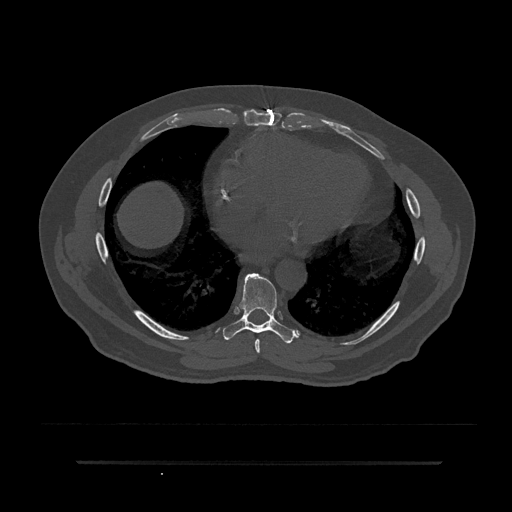
CT including the spine, one axial slice; slice 436 of 797 in the series (ordered by position); 120 kVp; bone window (W 1800 / L 400 HU); 0.5 mm slice thickness; 512 × 512 image matrix, field of view 464 × 464 mm. Patient: male, 59 years. Case-level facts recorded for this patient, not image findings: primary cancer: bile ducts.
Annotated regions visible in this slice (semi-automatic segmentation, software-assisted and operator-edited):
- T7 vertebra: bounding box (x1, y1, x2, y2) in pixels: (255, 339, 260, 353)
- T8 vertebra: (223, 273, 296, 344)